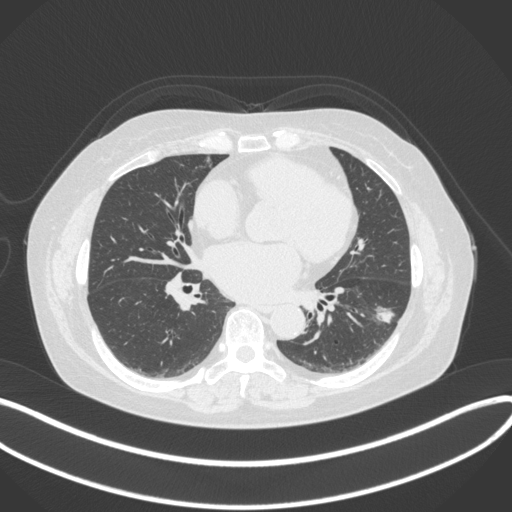
Chest CT, one axial slice. Position 163 of 373 along the scan axis. Reconstruction kernel B31f. Lung window (W 1500 / L -600 HU). 512 × 512 image matrix, field of view 400 × 400 mm. Patient: female, 67 years. From the clinical record (not read from this slice): clinical TNM (as recorded): T1c N0 M0.
Outlined on this slice (rectangle marked by the reading radiologist):
- lung tumour (recorded histology: adenocarcinoma): bounding box [x1, y1, x2, y2] px = [373, 303, 401, 330]